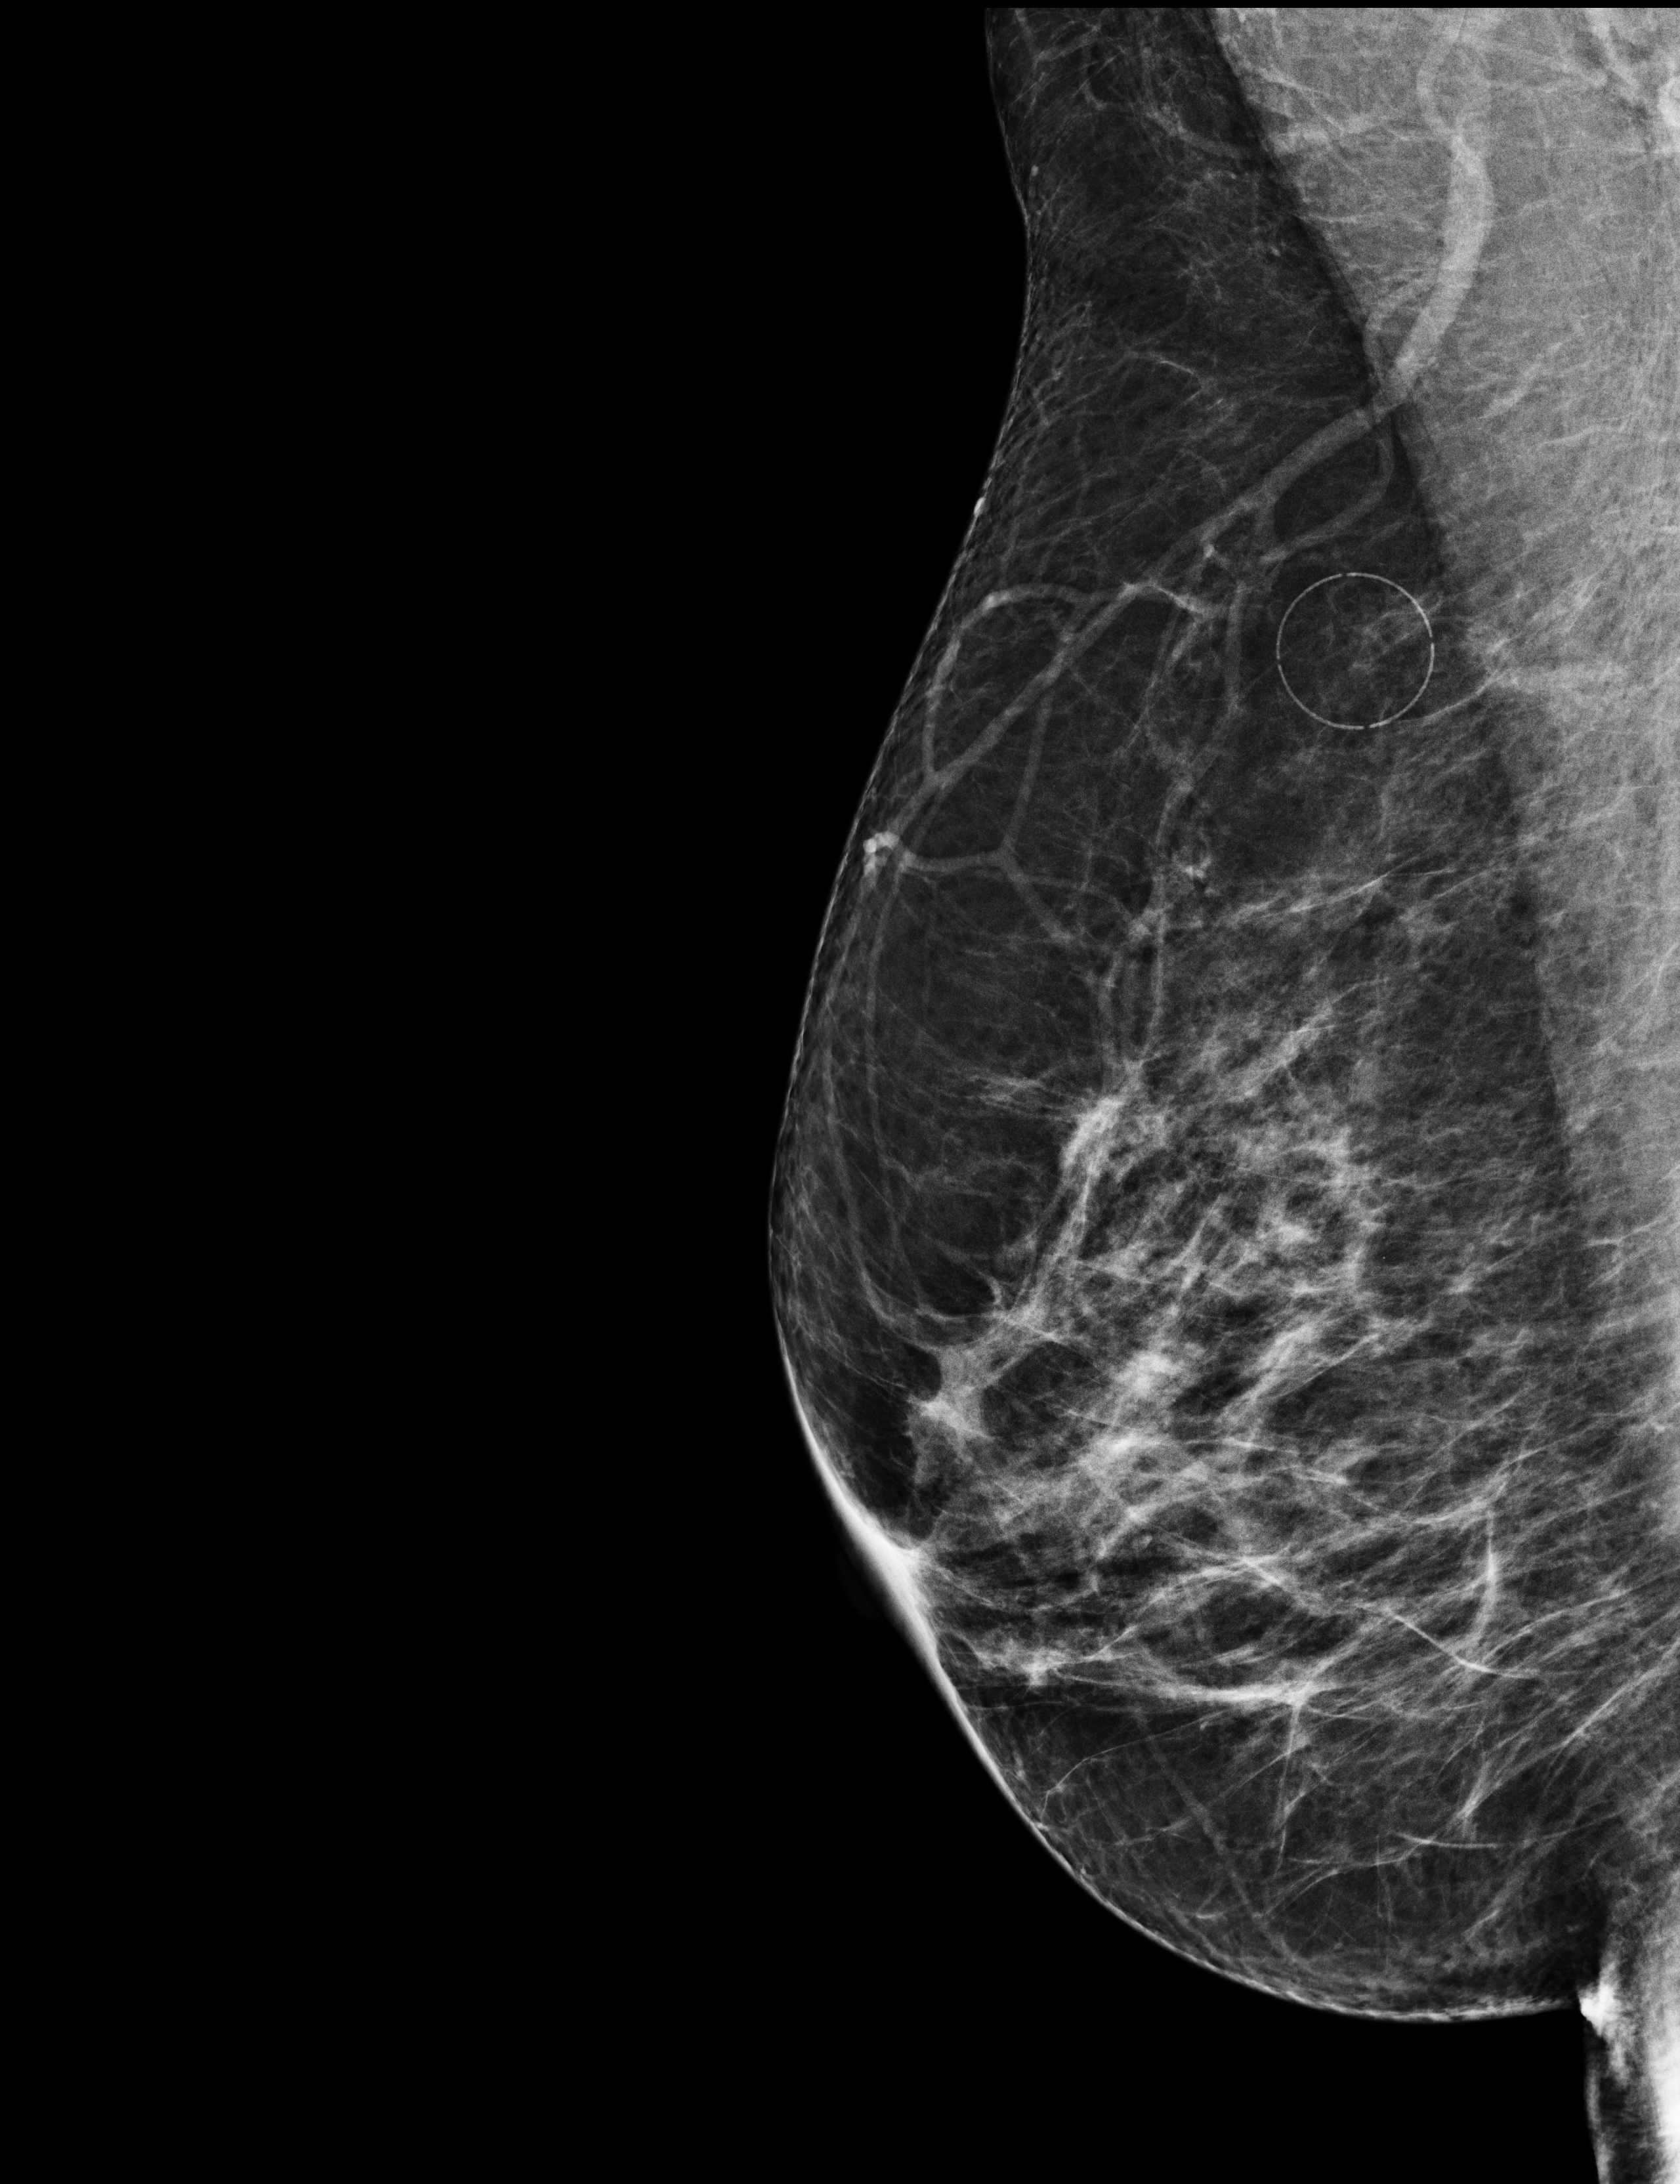
Annual screening mammography examination, system: Selenia Dimensions. Patient: female, 61 years.
Image type: full-field digital mammogram. Breast: right. Projection: MLO view.